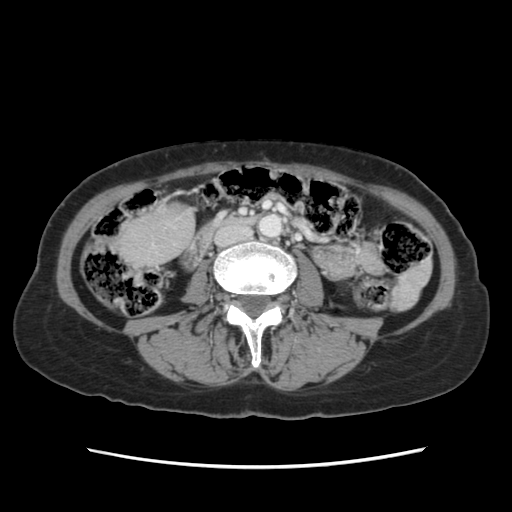
Contrast-enhanced abdominal CT, one axial slice. Position 16 of 120 along the scan axis. Intravenous contrast given. Soft-tissue window (W 400 / L 40 HU). 512 × 512 image matrix, field of view 330 × 330 mm. Female patient, age 70 years. From the clinical record (not read from this slice): diagnosis: colorectal cancer liver metastases, imaged before liver resection; multiple liver metastases: no; largest metastasis: 2.5 cm; chemotherapy before resection: yes.
Outlined on this slice (expert manual segmentation):
- liver: bounding box (x1, y1, x2, y2) in pixels: (119, 208, 190, 263)
- planned liver remnant (the part of the liver to remain after resection): (119, 208, 191, 263)